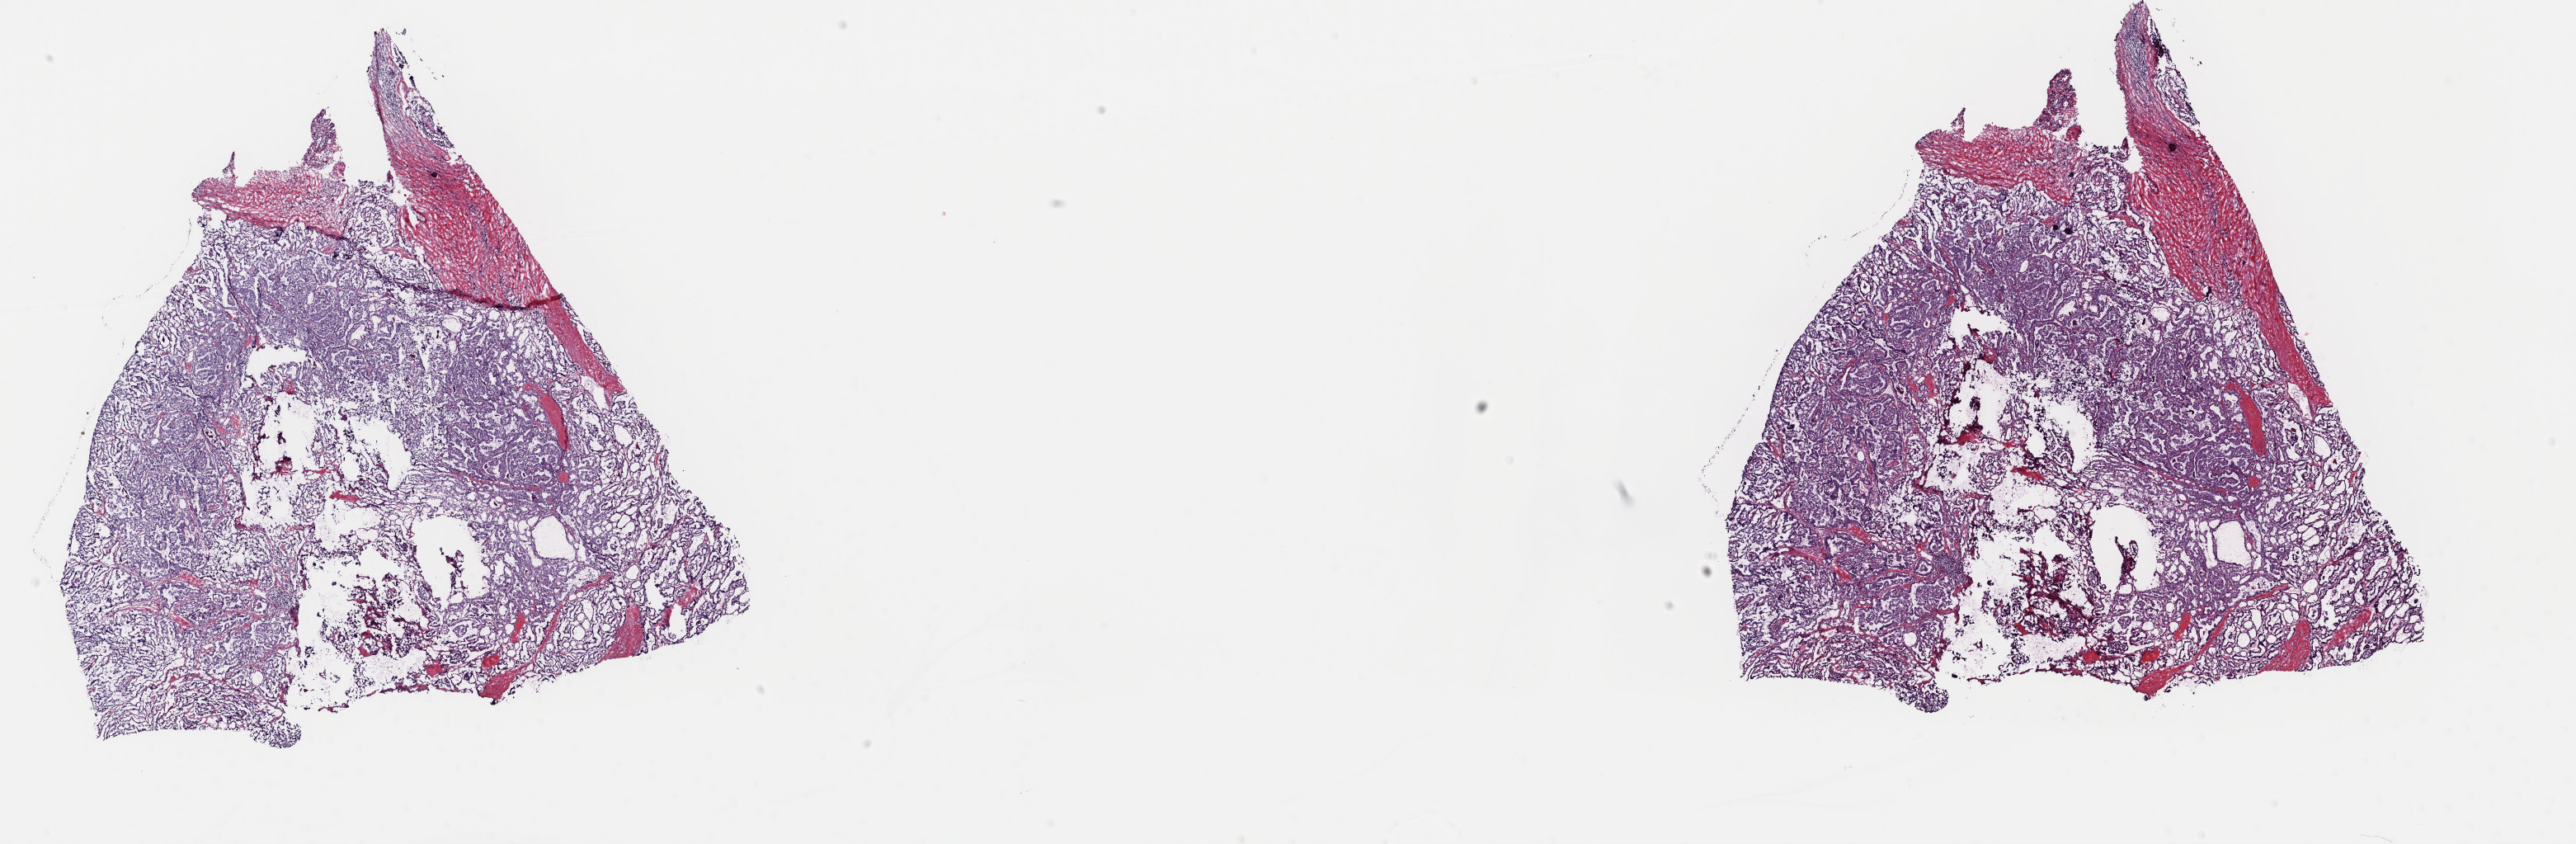
H&E-stained whole-slide image, shown as a low-resolution overview of the whole scanned area (about 24.7 x 8.1 mm); frozen section from the top of the tissue portion; primary tumour sample from the thyroid. Female, age 26 years at initial diagnosis. Composition of this section per pathologist review: tumour cells 90%, tumour nuclei 95%, normal cells 0%, stromal cells 10%, necrosis 0%. Inflammatory infiltration, as recorded: lymphocyte infiltration 1%, monocyte infiltration 0%, neutrophil infiltration 0%.
* lymph nodes positive (case pathology): 3 of 15 examined
* histologic diagnosis: Papillary adenocarcinoma, NOS (thyroid gland)
* AJCC pathologic stage: I